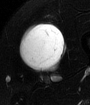
MRI of an extremity soft-tissue mass, one axial slice; slice 38 of 65 in the series (ordered by position); T2-weighted fat-saturated; MR volume resampled by the dataset authors to the PET/CT grid (not the native acquisition matrix); 3.27 mm slice thickness; 90 × 105 image matrix, field of view 88 × 103 mm. Male patient. From the clinical record (not read from this slice): histological type: mixoid liposarcoma; grade: low; site of the primary tumour: left thigh.
Structures marked on this image (expert contour drawn on MRI and transferred to this co-registered scan by the dataset authors):
- gross tumour volume (mass): bounding box [x1, y1, x2, y2] px = [18, 23, 63, 70]